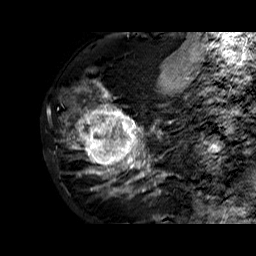
Breast MRI (dynamic contrast-enhanced), one sagittal slice; slice 24 of 60 in the series (ordered by position); dynamic contrast-enhanced series, time point 2 of 6 at this slice position (early post-contrast); 1.5 T; TE 6.3 ms, TR 32.4 ms; 4 mm slice thickness; 256 × 256 image matrix. Female patient. From the clinical record (not read from this slice): setting: breast cancer imaged before/during neoadjuvant chemotherapy; receptor status: HR-positive, HER2-negative.
Outlined on this slice (semi-automatic segmentation, software-assisted and operator-edited):
- analysis volume of interest (the breast-tissue region the enhancement analysis was run in; not a lesion): bounding box [x1, y1, x2, y2] px = [68, 72, 177, 183]
- tumour enhancement mask (voxels above the 100 % enhancement threshold inside the analysis volume of interest): [79, 87, 167, 183]